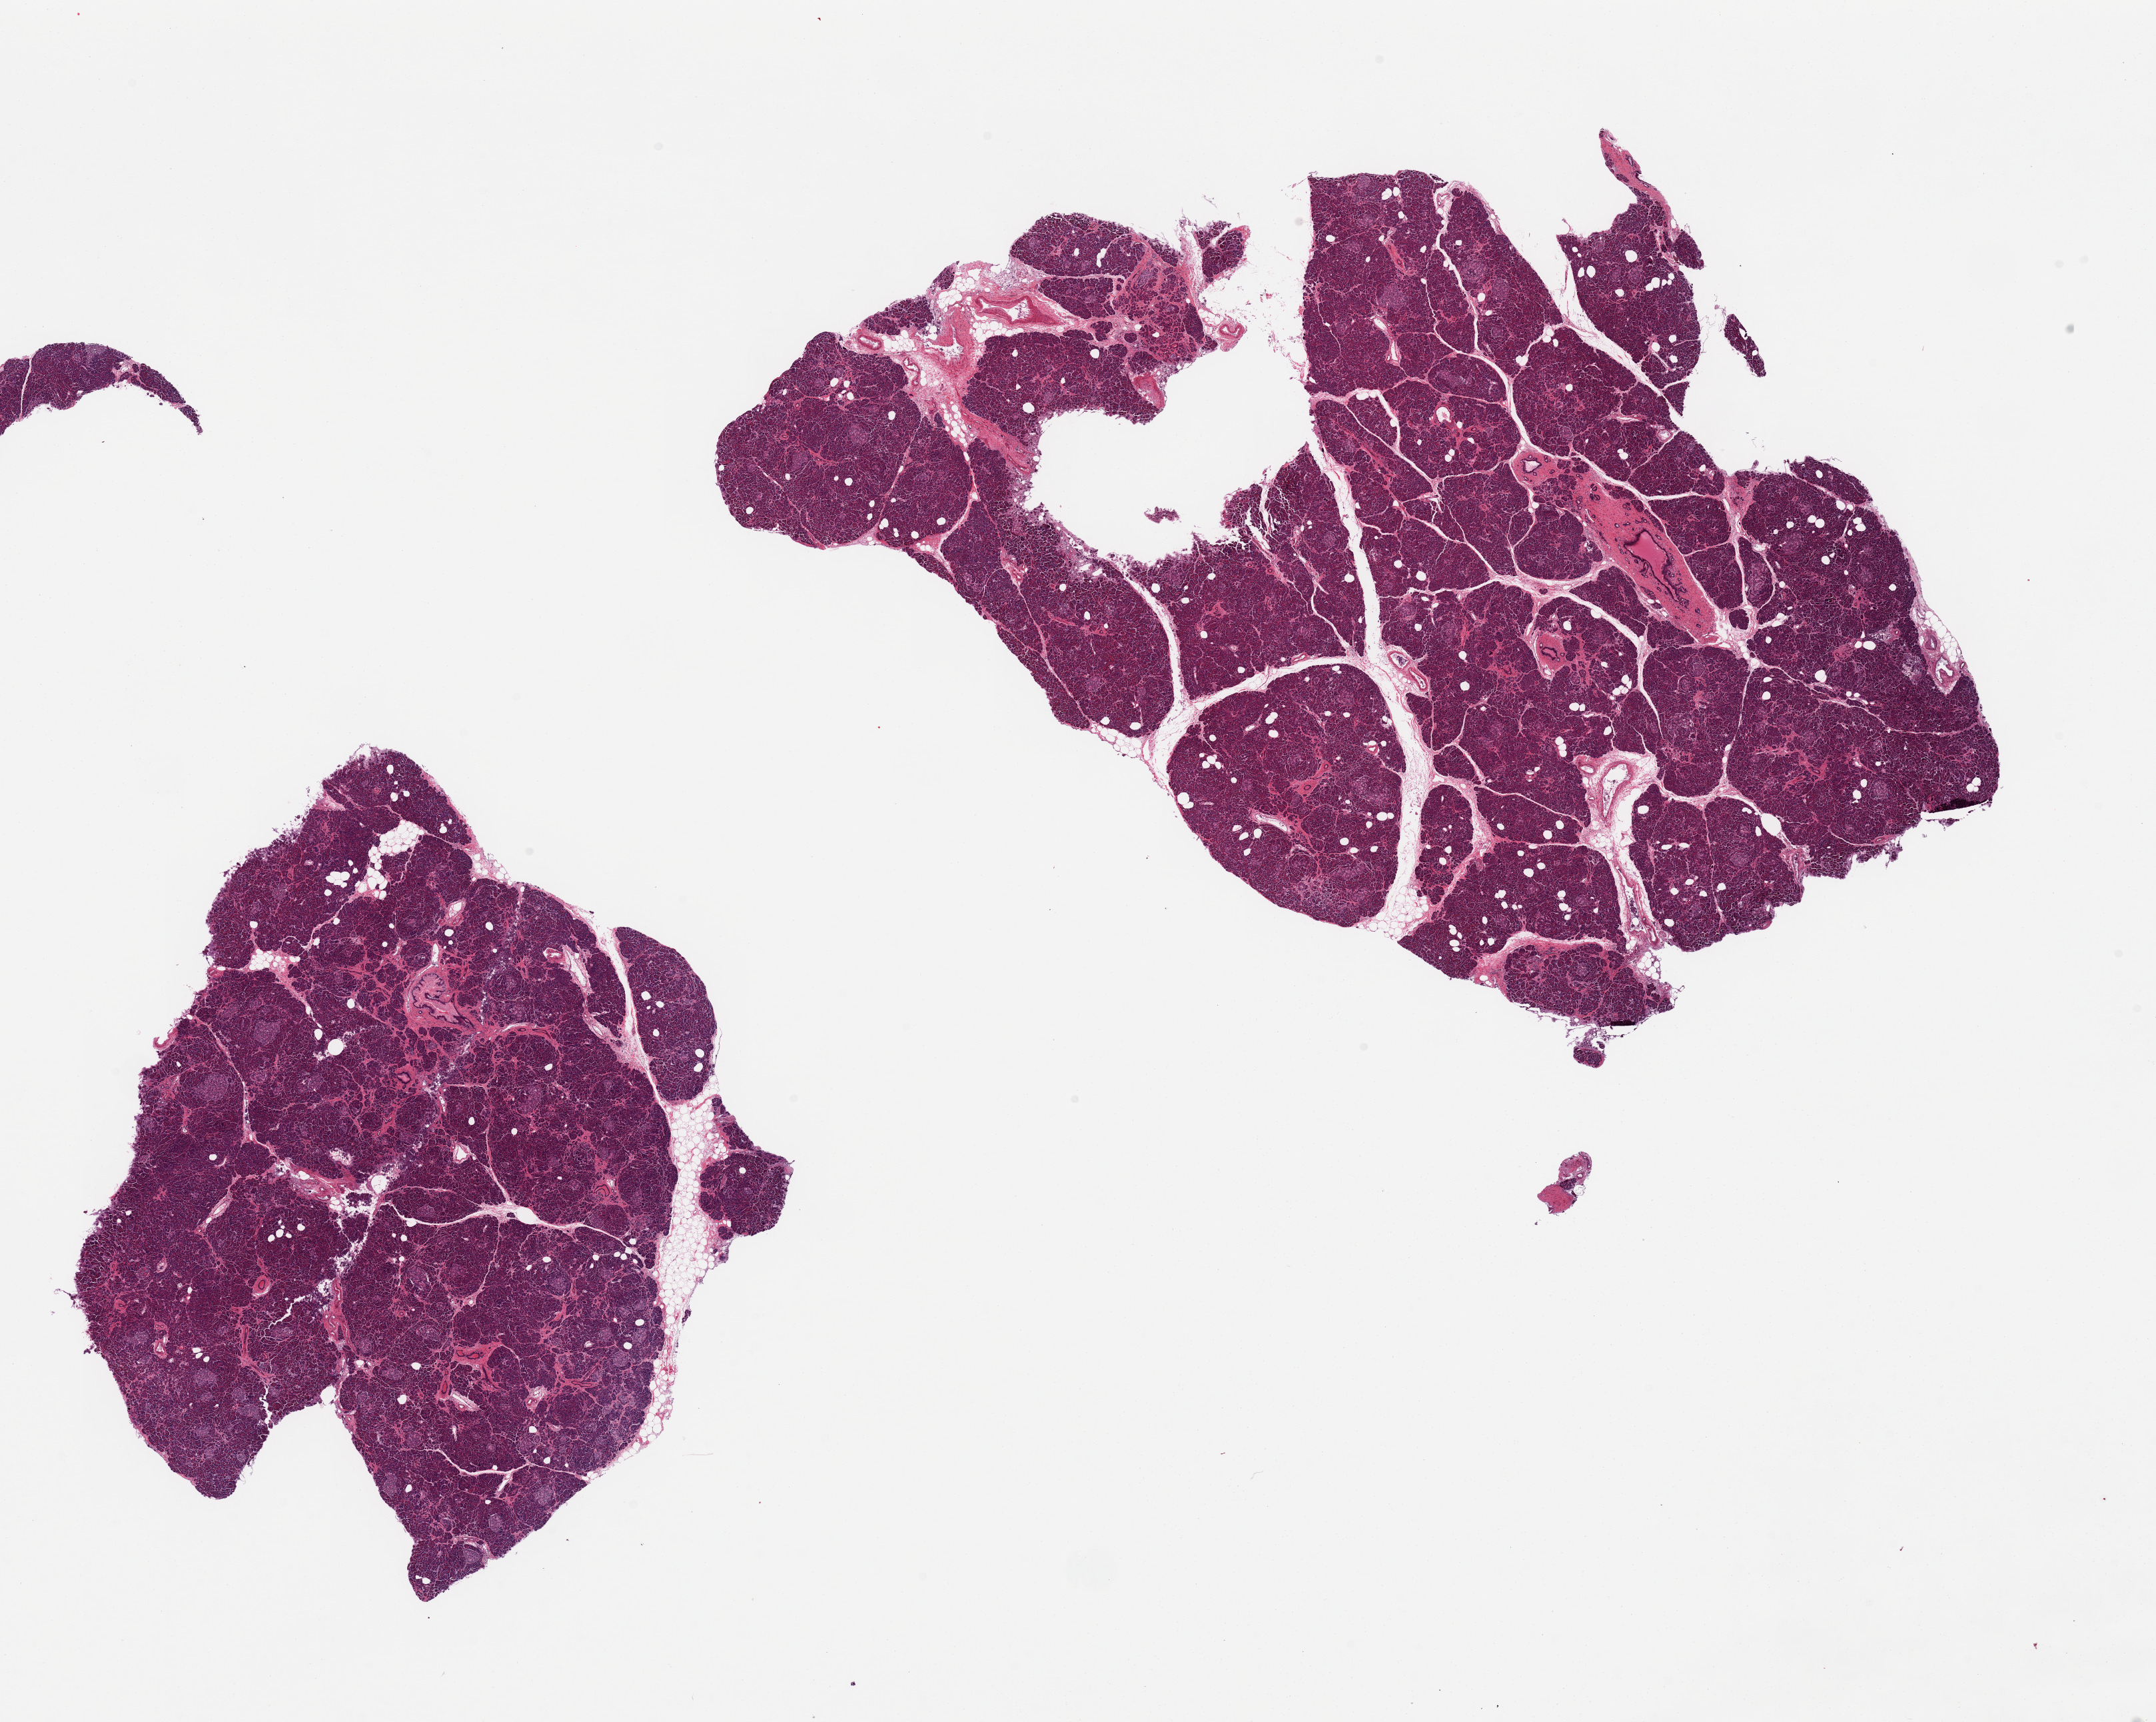
Whole-slide image, hematoxylin and eosin (H&E) stain, brightfield — whole scanned area (about 25.6 x 20.4 mm, slide scanned at 20x) shown as a low-resolution overview, PAXgene-fixed, paraffin-embedded tissue, section of pancreas (target tissue), donor tissue sample.
Review note (as recorded): 2 pieces, well preserved, Islets well visualized.